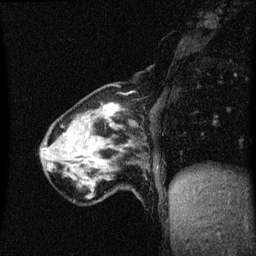
Breast MRI (dynamic contrast-enhanced), one sagittal slice; position 16 of 60 along the scan axis; dynamic contrast-enhanced series, image 2 of 3 at this slice position (ordered by acquisition); 1.5 T; TE 4.2 ms, TR 8.4 ms; 256 × 256 image matrix, field of view 200 × 200 mm. Female patient, age 64 years. Case-level facts recorded for this patient, not image findings: setting: breast cancer imaged before/during neoadjuvant chemotherapy; receptor status: HR-positive, HER2-negative.
Structures marked on this image (semi-automatically segmented with operator editing):
- analysis volume of interest (the breast-tissue region the enhancement analysis was run in; not a lesion): box from (x=56, y=106) to (x=134, y=175) px
- tumour enhancement mask (voxels above the 70 % enhancement threshold inside the analysis volume of interest): (x=106, y=106)–(x=117, y=115)